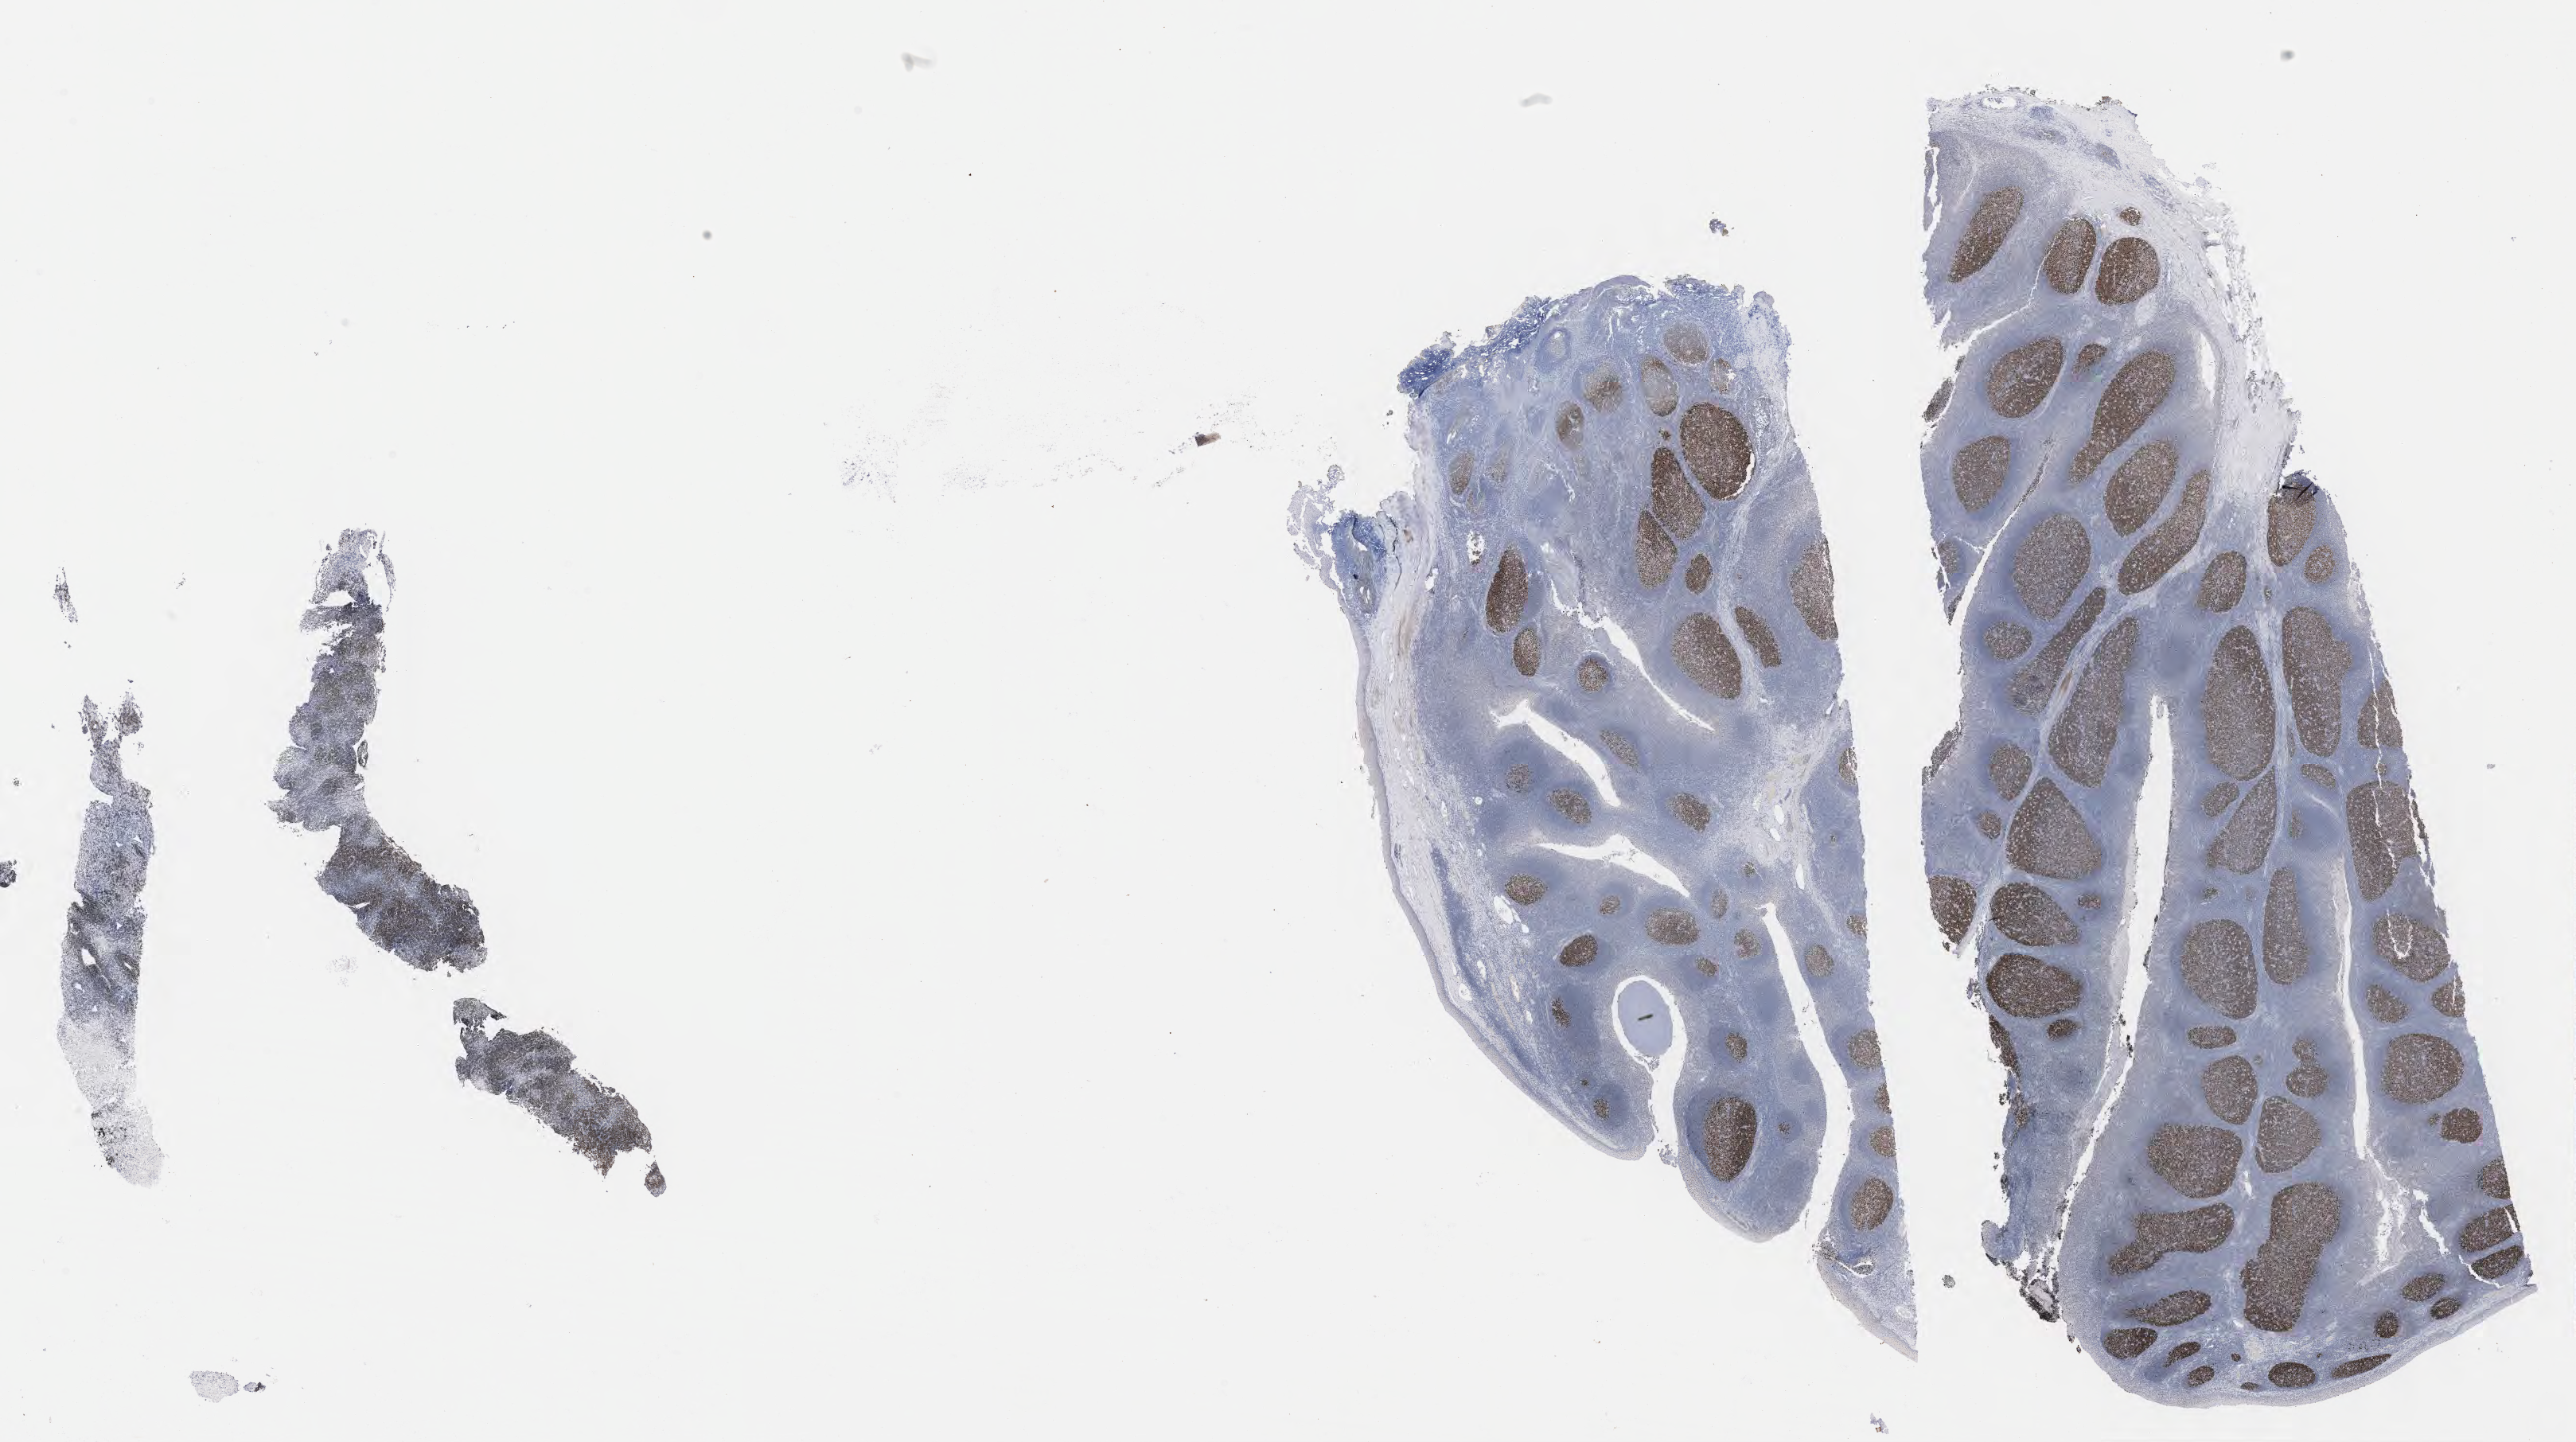
Whole-slide image, immunohistochemical stain for BCL6 — a low-resolution overview of the entire scanned area, about 26.2 x 14.6 mm; tumor tissue. Patient female; 12 years old.
Histologic diagnosis: Burkitt lymphoma, NOS.